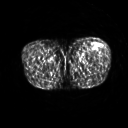
FDG PET of an extremity soft-tissue mass (from a PET/CT study), one axial slice. Slice 216 of 267 in the series (ordered by position). 3.27 mm slice thickness. 128 × 128 image matrix, field of view 500 × 500 mm. Male patient, age 64 years. From the clinical record (not read from this slice): histological type: extraskeletal osteosarcoma; grade: high; site of the primary tumour: thigh.
Outlined on this slice (expert contour drawn on MRI and transferred to this co-registered scan by the dataset authors):
- gross tumour volume (mass): bounding box [x1, y1, x2, y2] px = [97, 44, 99, 49]